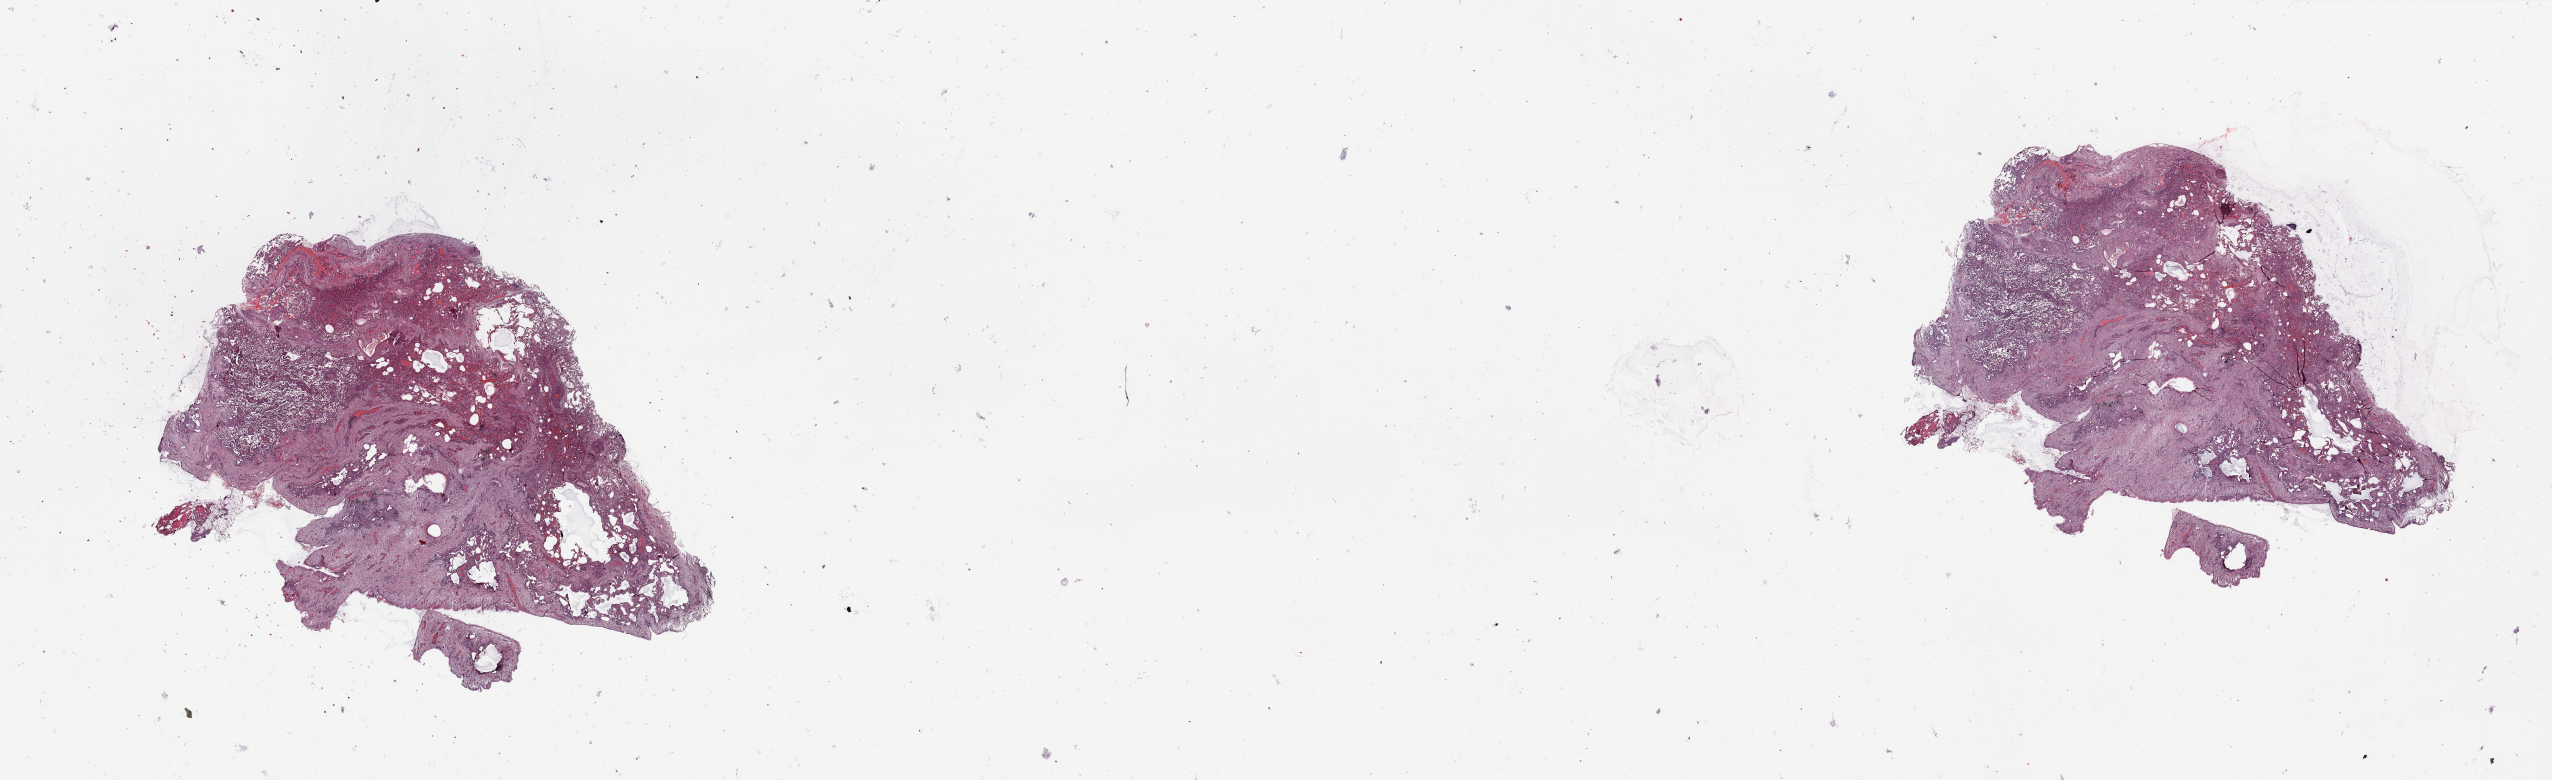
Whole-slide histology image, Hematoxylin and eosin (H&E) stained, a low-resolution overview of the entire scanned area, about 40.4 x 12.3 mm (slide scanned at 20x), normal (non-tumour) tissue sample, lung. Male, 66 y/o.
* this section: normal (non-tumour) tissue from the same patient
* patient diagnosis: Squamous cell carcinoma, NOS